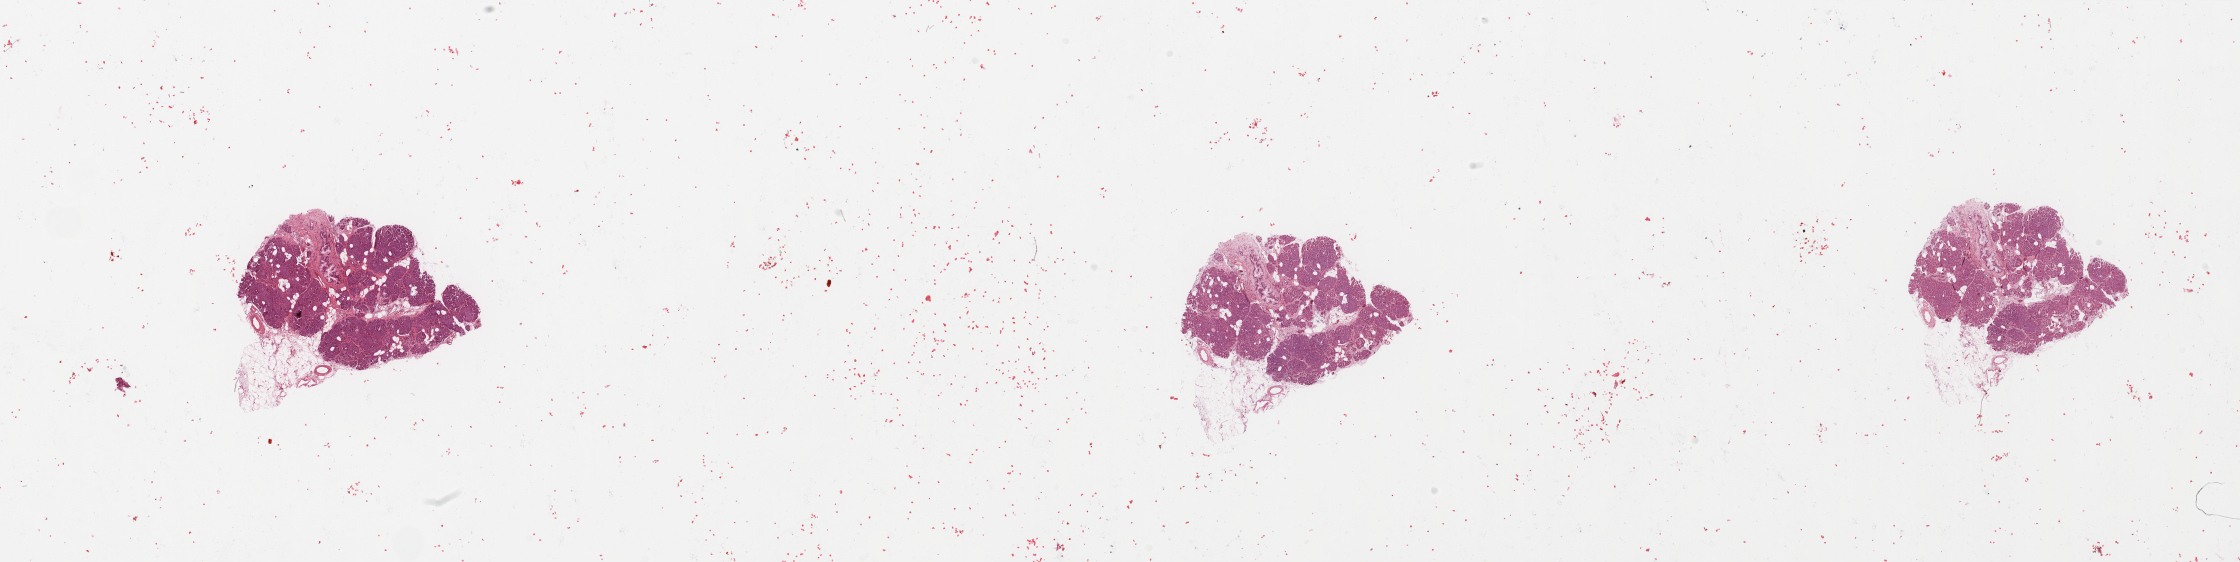
H&E-stained whole-slide image — shown as a low-resolution overview of the whole scanned area (about 35.4 x 8.9 mm), normal (non-tumour) tissue sample, pancreas. Female, 63 y/o.
This section: normal (non-tumour) tissue from the same patient. Patient diagnosis: Infiltrating duct carcinoma, NOS.